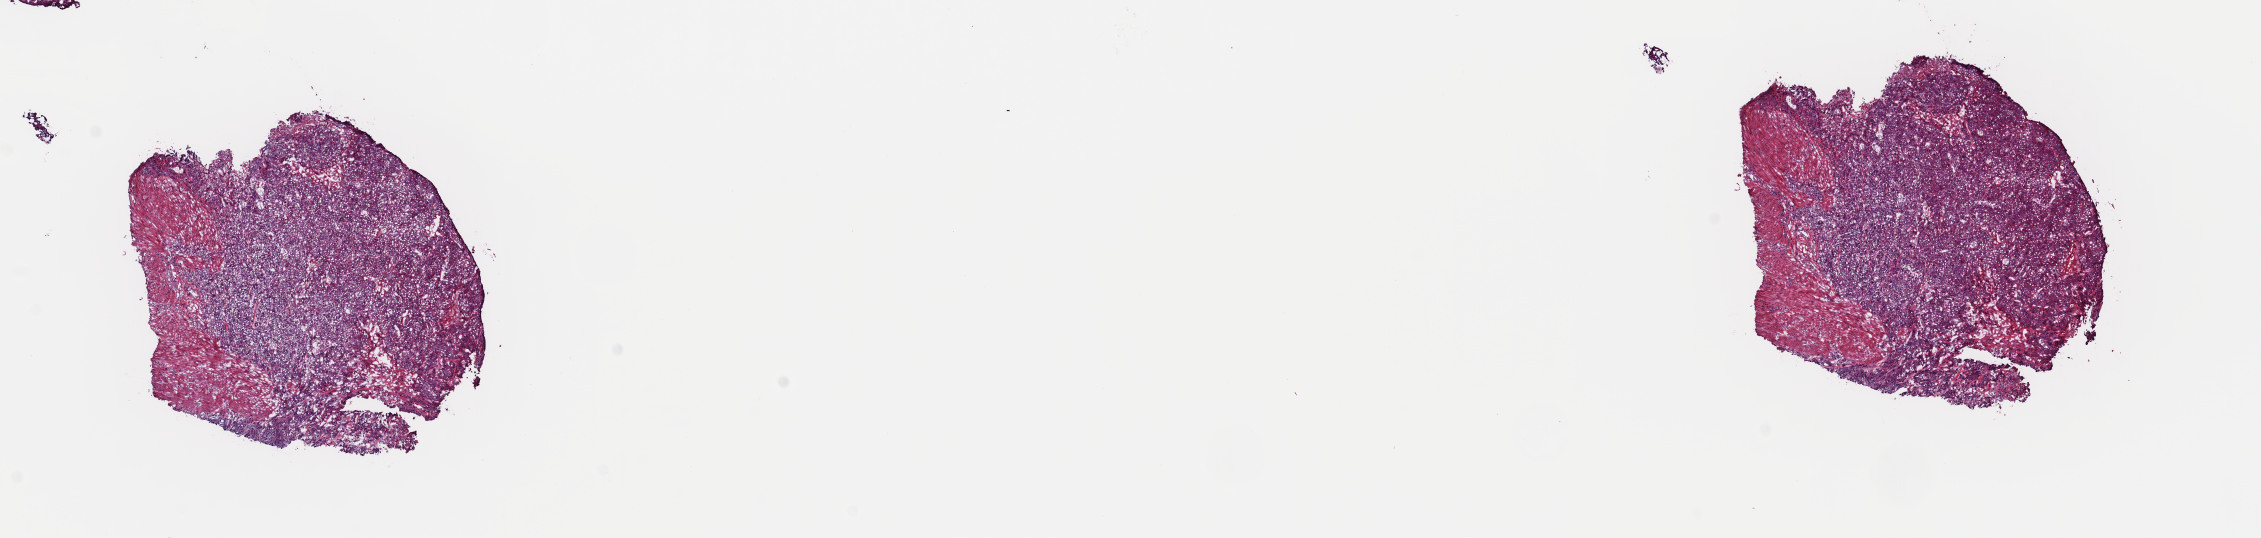
Digitized Hematoxylin and eosin (H&E) stained tissue section (whole slide) — low-resolution overview of the scanned area, about 17.9 x 4.2 mm (slide scanned at 40x), frozen section from the top of the tissue portion, sample: primary tumour, bladder. Patient: male, age at initial diagnosis 69 years. Histologic grade: high grade. Composition of this section per pathologist review: tumour cells 80%, tumour nuclei 80%, normal cells 0%, stromal cells 13%, necrosis 7%. Infiltration values recorded for this section: lymphocyte infiltration 2%, monocyte infiltration 1%, neutrophil infiltration 1%.
* pathologic diagnosis: Transitional cell carcinoma (posterior wall of bladder)
* AJCC pathologic stage: II (7th edition)